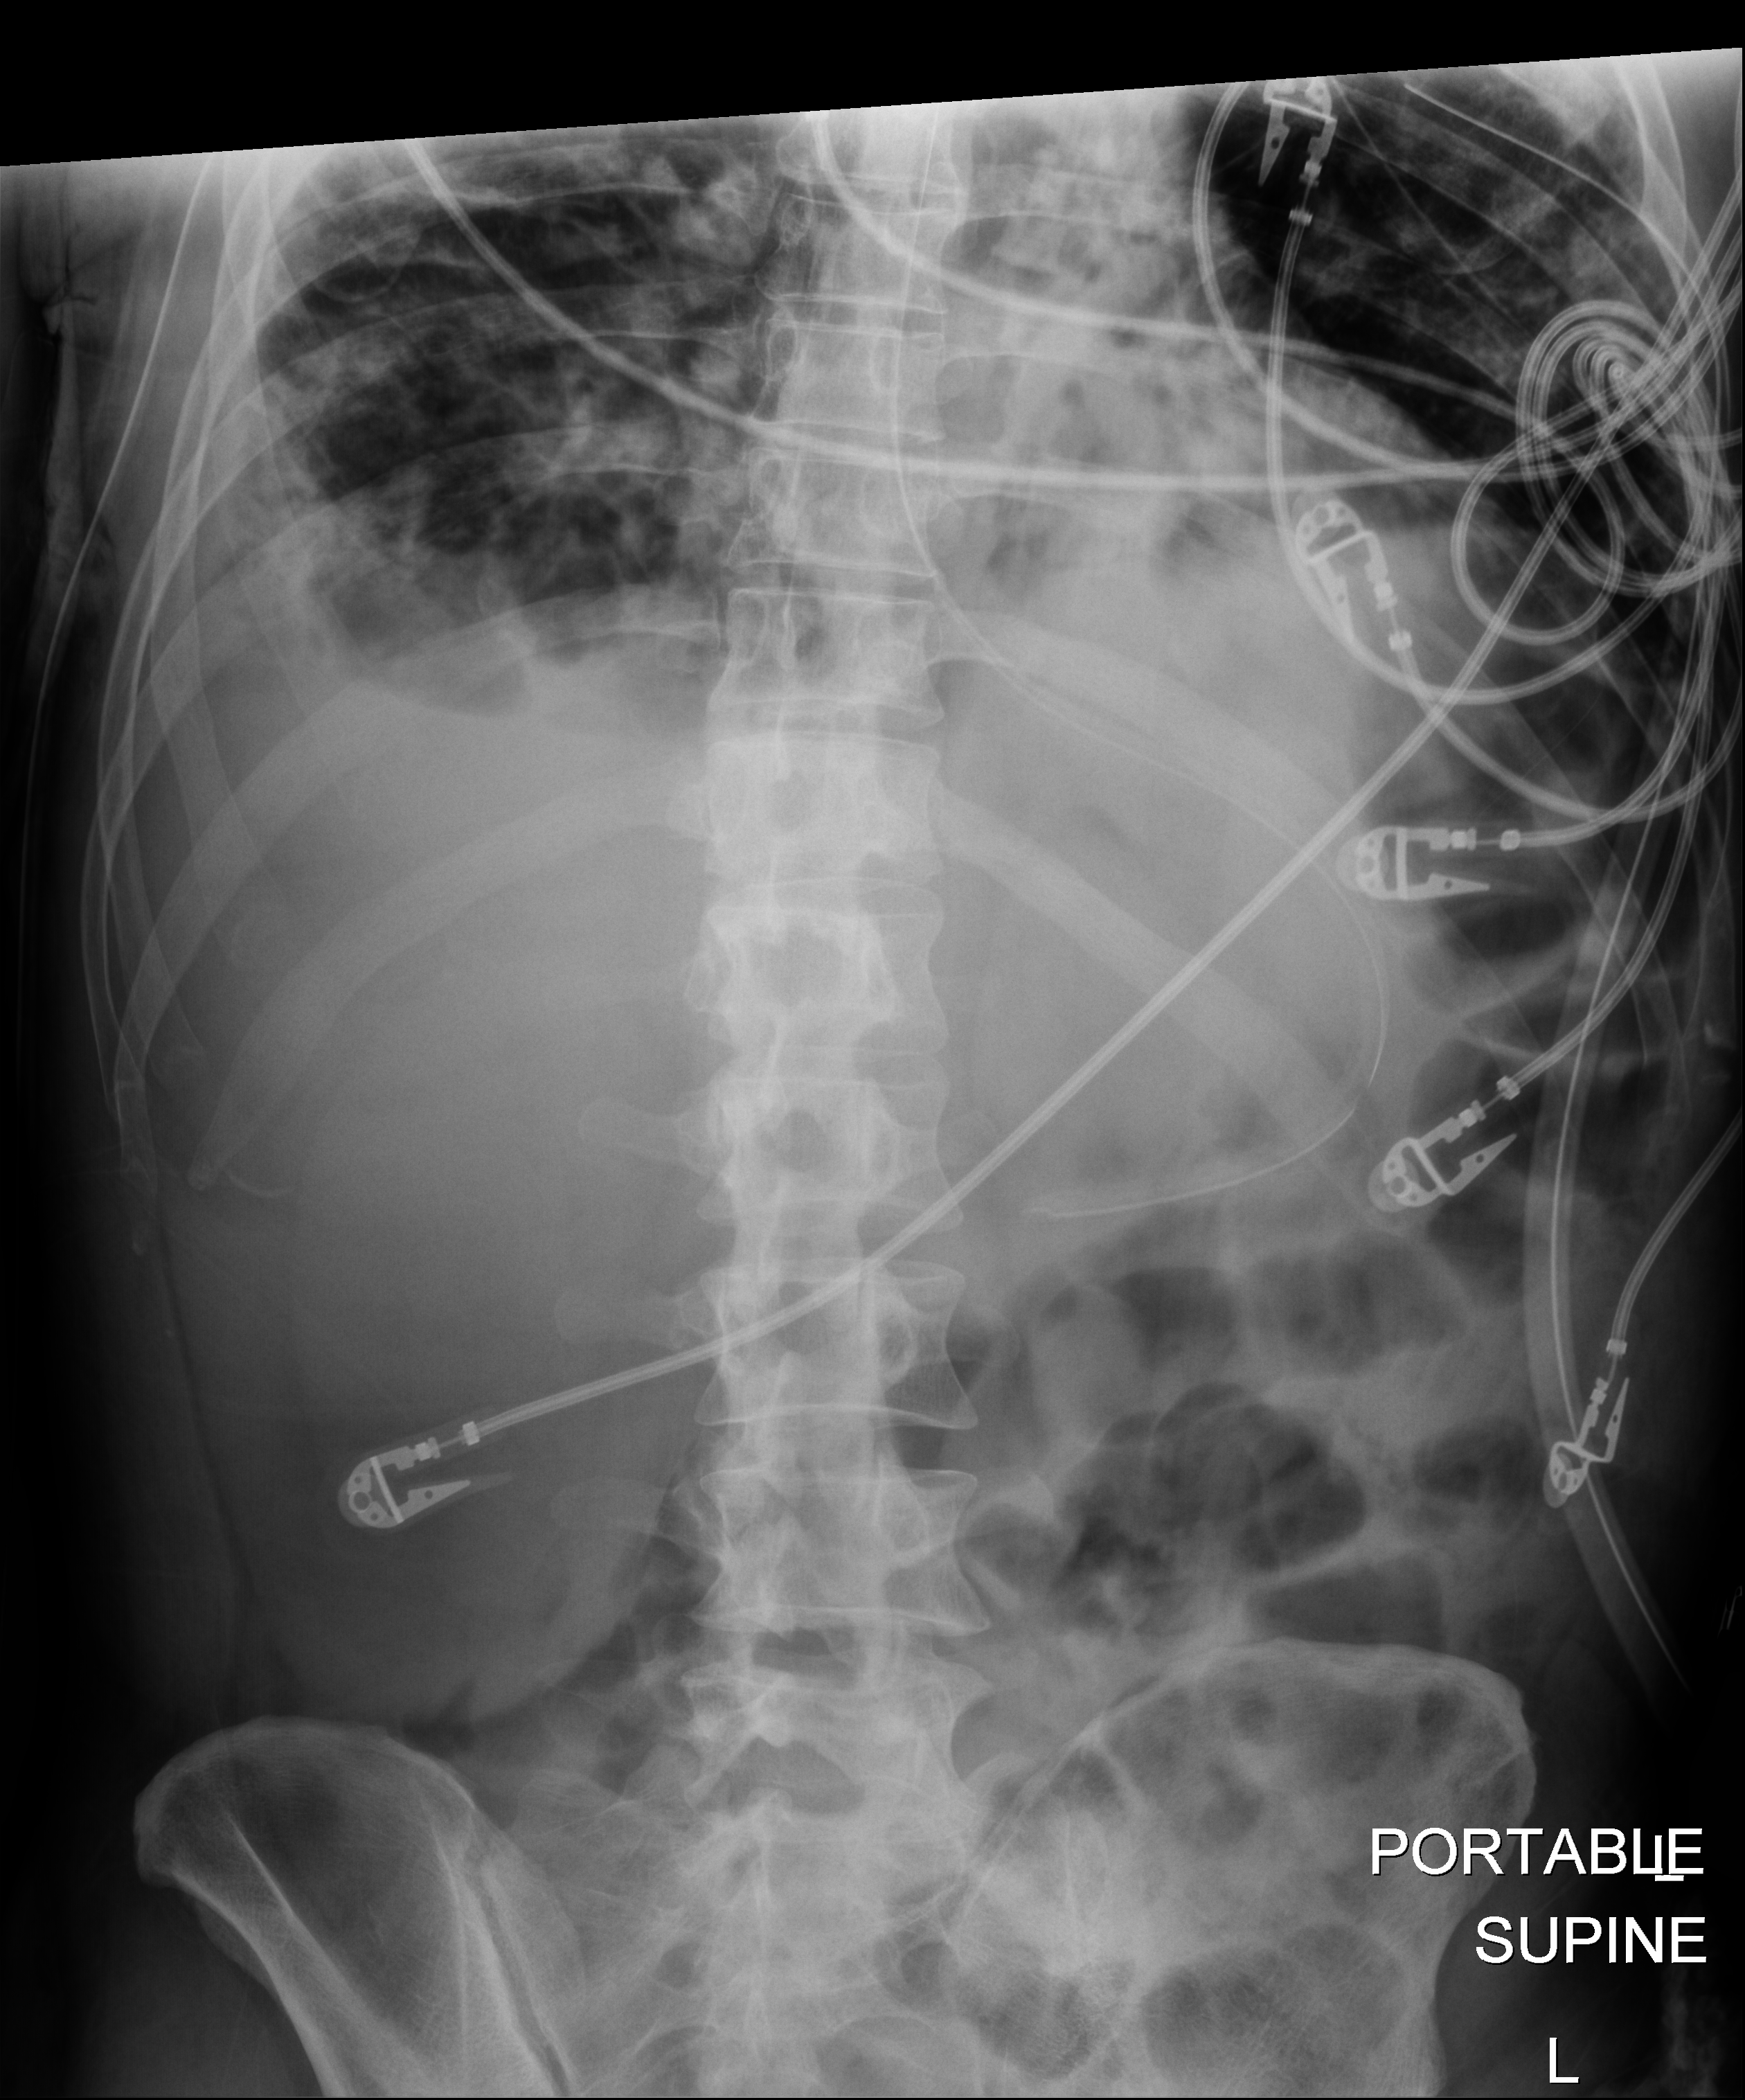
Bedside abdomen radiograph (digital radiography). Patient hospitalised with COVID-19; male, aged 18–59 years.
Hospital-stay facts (about this admission, not read from this image; timing relative to this image not recorded): diabetes (admission record): yes.